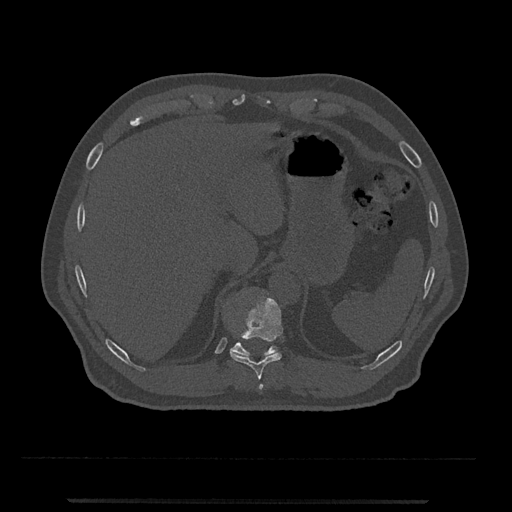
CT including the spine, one axial slice; reconstruction kernel Br40s/3; 120 kVp; bone window (W 1800 / L 400 HU); 0.5 mm slice thickness; 512 × 512 image matrix. Patient: male, 63 years. From the clinical record (not read from this slice): primary cancer: prostate.
Annotated regions visible in this slice (semi-automatic segmentation, software-assisted and operator-edited):
- T10 vertebra: bounding box [x1, y1, x2, y2] px = [230, 296, 283, 380]
- T11 vertebra: [230, 342, 278, 356]
- T9 vertebra: [259, 384, 264, 390]